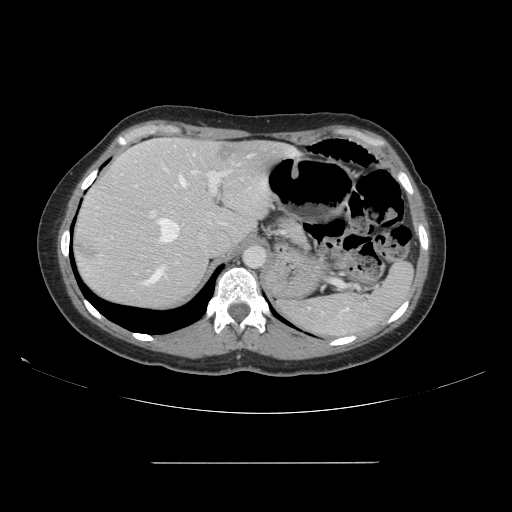
Contrast-enhanced abdominal CT, one axial slice. Position 114 of 151 along the scan axis. 120 kVp. Intravenous contrast given. Soft-tissue window (W 400 / L 40 HU). 2.5 mm slice thickness. 512 × 512 image matrix. Female patient, age 46 years. From the clinical record (not read from this slice): diagnosis: colorectal cancer liver metastases, imaged before liver resection; multiple liver metastases: yes; largest metastasis: 3 cm; disease in both lobes: yes.
Annotated regions visible in this slice (expert manual segmentation):
- hepatic veins: bounding box <151,154,252,243> (left, top, right, bottom; pixels)
- liver: <73,139,293,309>
- planned liver remnant (the part of the liver to remain after resection): <88,138,290,252>
- portal vein (with intrahepatic branches): <135,171,227,285>
- liver metastasis: <75,240,98,261>
- liver metastasis: <218,145,239,162>